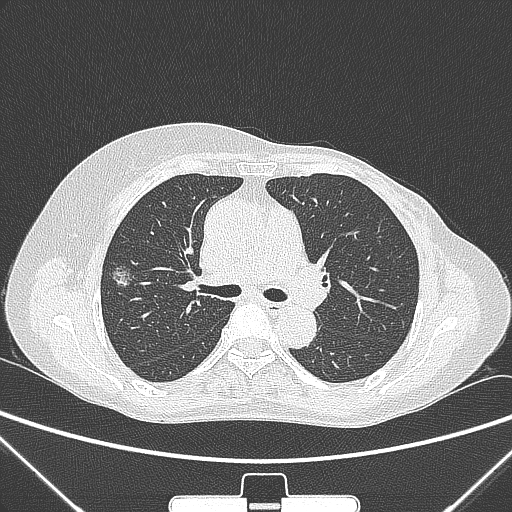
Chest CT, one axial slice. Slice 158 of 265 in the series (ordered by position). 120 kVp. Lung window (W 1500 / L -600 HU). 1 mm slice thickness. 512 × 512 image matrix, field of view 350 × 350 mm. Patient: female, 64 years. From the clinical record (not read from this slice): clinical TNM (as recorded): T1c N0 M0; histopathological grade: G1-2.
Annotated regions visible in this slice (rectangle marked by the reading radiologist):
- lung tumour (recorded histology: adenocarcinoma): box from (x=102, y=260) to (x=139, y=292) px